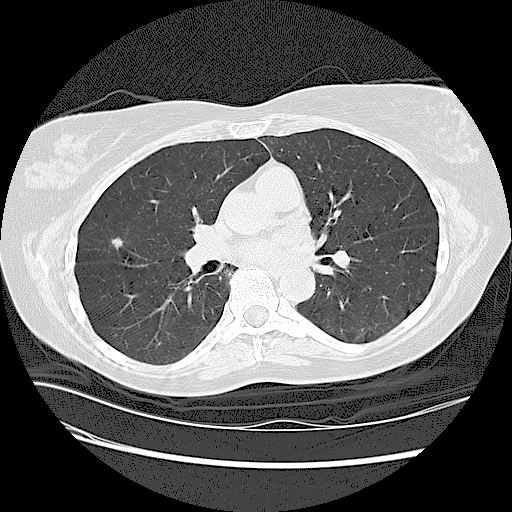
Low-dose screening chest CT, axial slice. Baseline annual screen. Lung window (W 1500 / L -600 HU). 2.5 mm slice thickness. Lung (sharp) reconstruction kernel (LUNG). Slice 62 of 125 in the series. Female participant, aged 63 years at enrolment.
• Expert reader's lesion annotation, bounding box <96,228,137,264> (left, top, right, bottom; pixels).
• Reader record for this screening exam (exam-level; its link to the box is not recorded): non-calcified nodule or mass ≥4 mm, right upper lobe, 7 × 7 mm, spiculated (stellate) margins, soft tissue attenuation.
• Official screen result: positive, change unspecified: nodule(s) >= 4 mm or enlarging nodule(s), mass(es), or other non-specific abnormalities suspicious for lung cancer.
• Lung cancer was diagnosed 69 days after this screen: adenocarcinoma, NOS, right upper lobe, well differentiated (G1), stage IA (AJCC 6th edition), 90 mm at pathology.